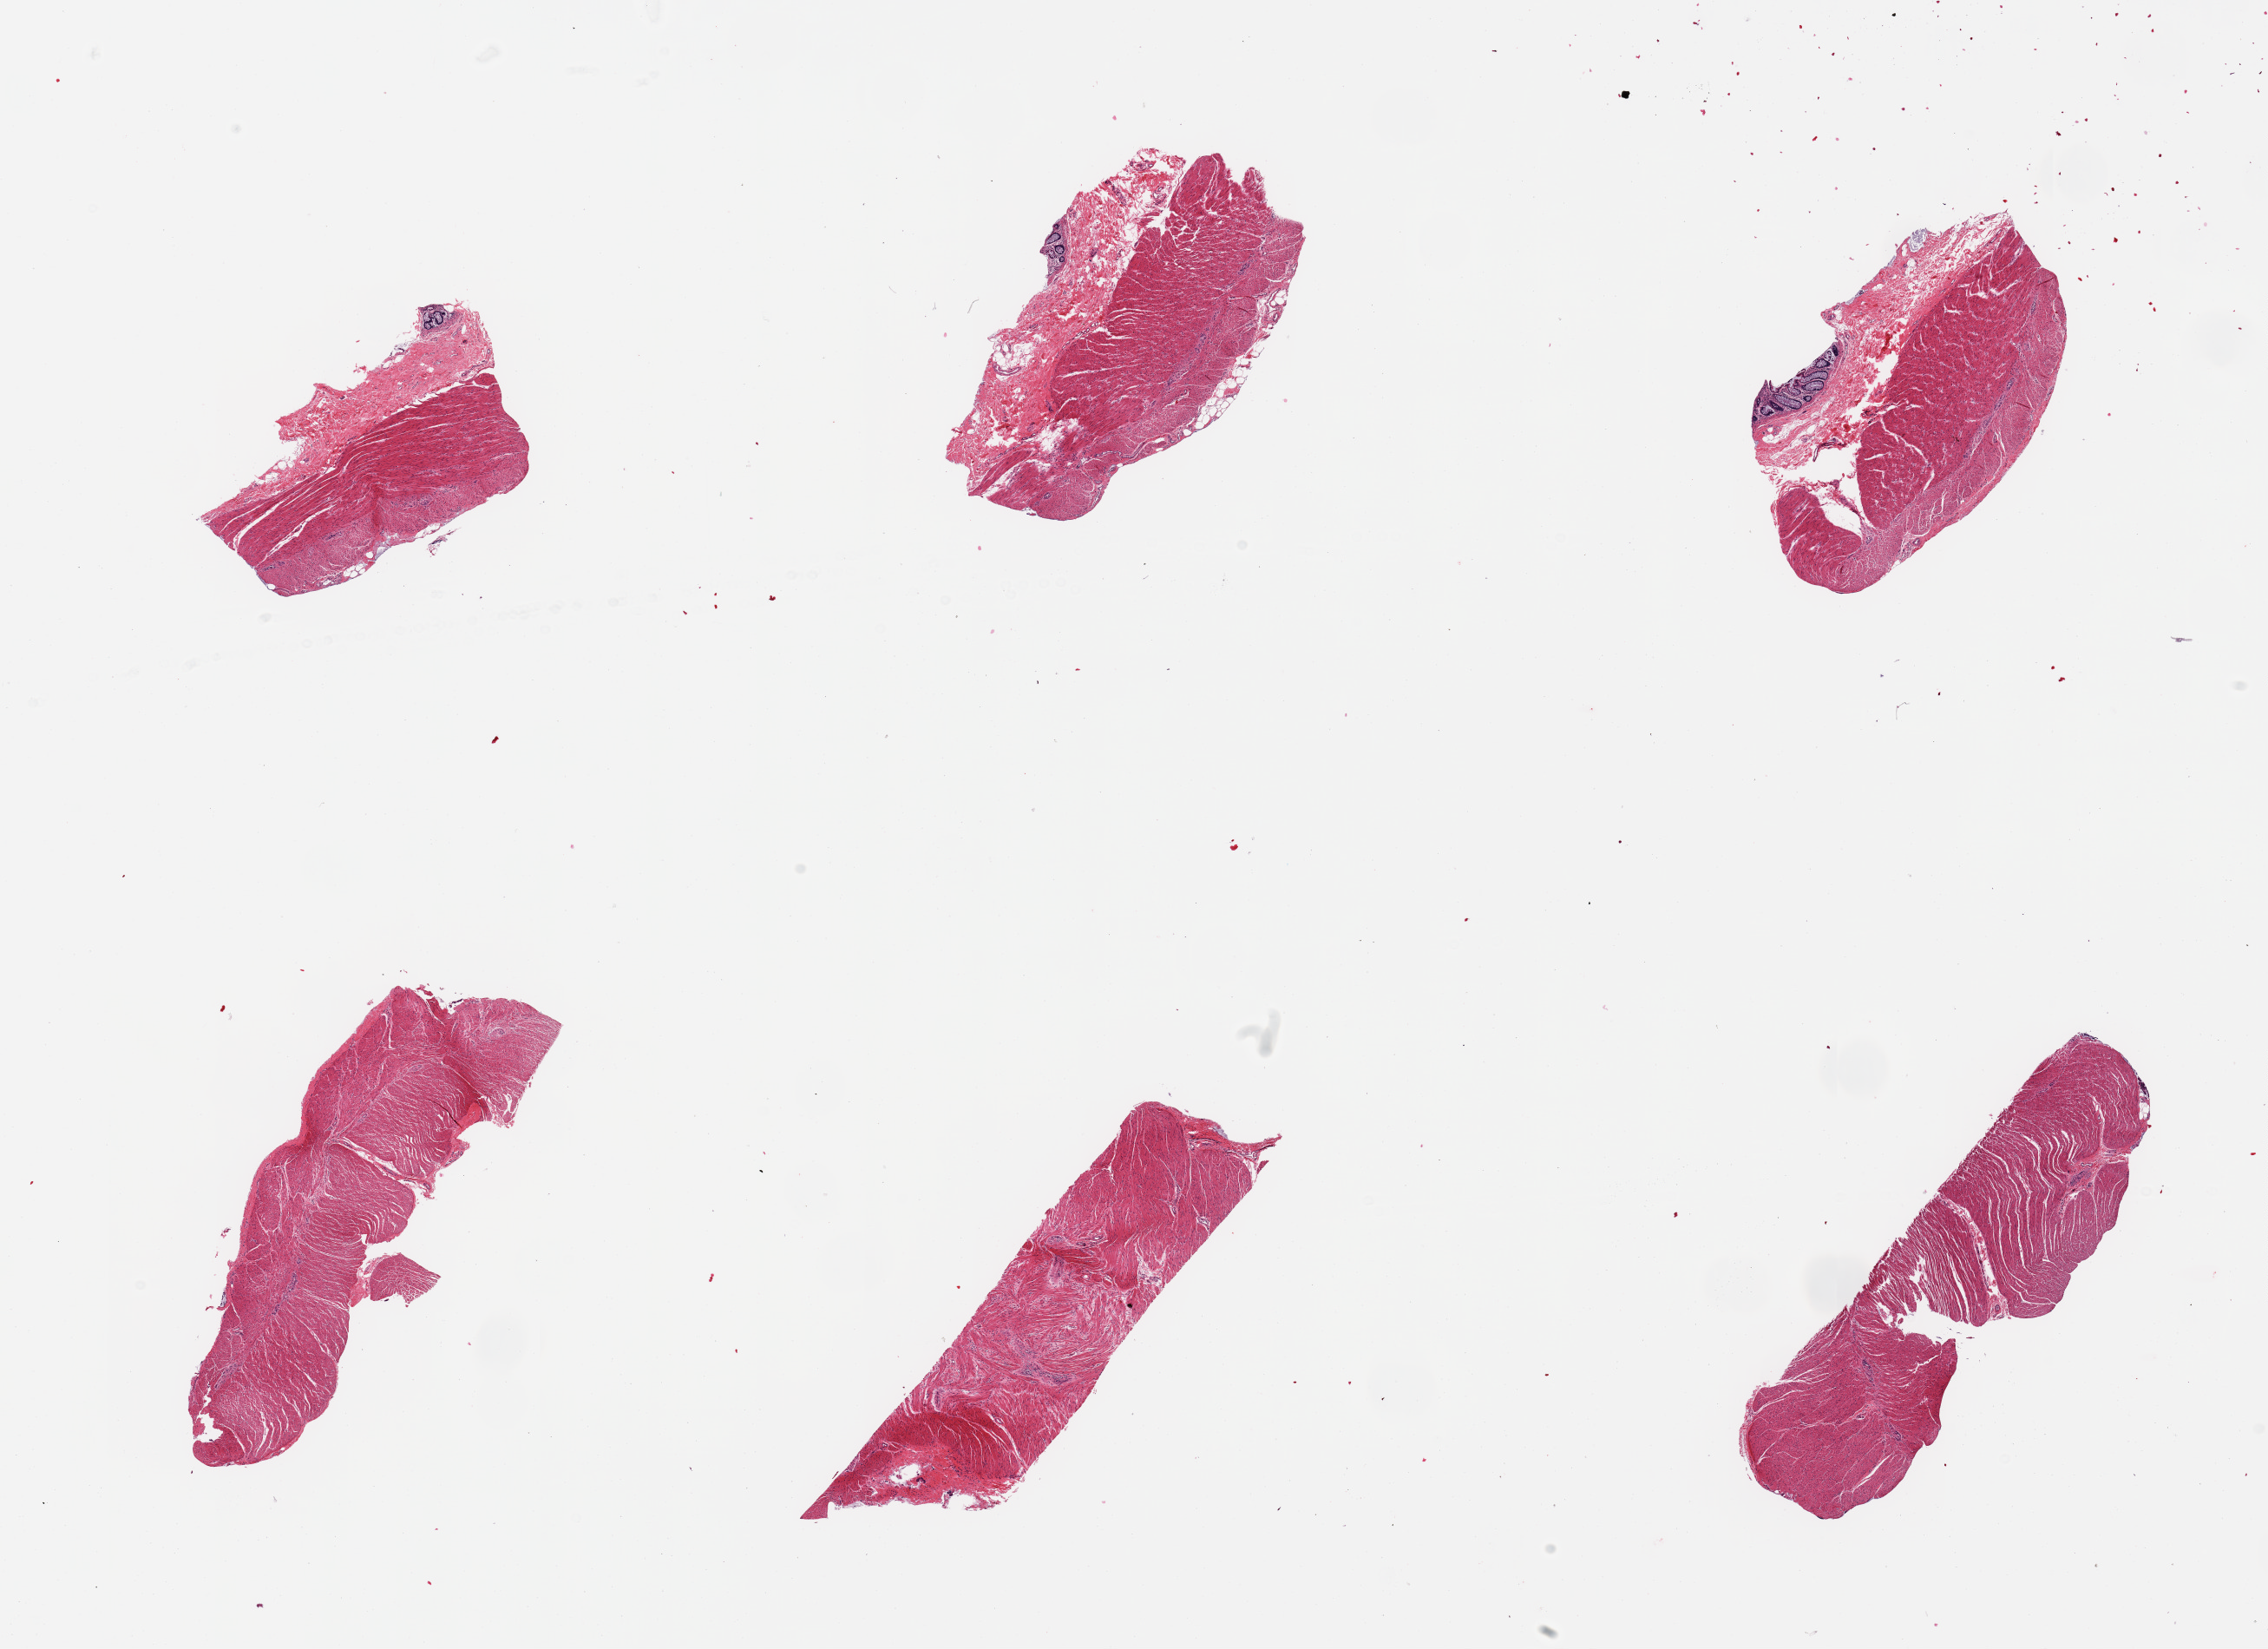
Whole-slide image, hematoxylin and eosin (H&E) stain — shown as a low-resolution overview of the whole scanned area (about 20.7 x 15.0 mm, acquisition: 20x scan), PAXgene-fixed, paraffin-embedded tissue, section of sigmoid colon (target tissue), tissue donor sample. Donor: male.
Pathologist's review note for this sample: 6 pieces, confirmed target muscularis, ~35% stroma & trace mucosa.